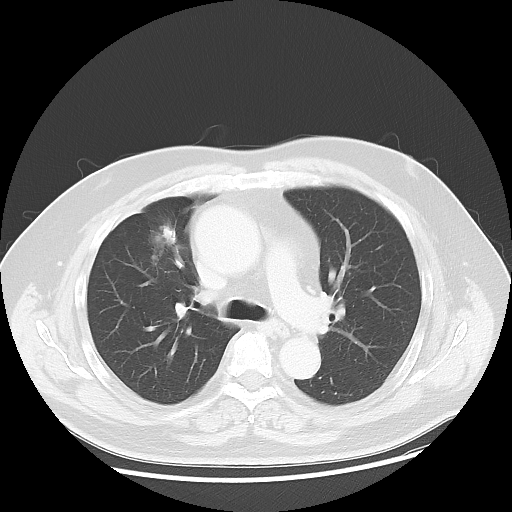
Chest CT, one axial slice. Position 29 of 48 along the scan axis. Lung window (W 1500 / L -600 HU). 512 × 512 image matrix. Male patient, age 60 years. Case-level facts recorded for this patient, not image findings: clinical TNM (as recorded): T2 N3 M0.
Structures marked on this image (rectangle marked by the reading radiologist):
- lung tumour (recorded histology: adenocarcinoma): bounding box (x1, y1, x2, y2) in pixels: (137, 212, 184, 268)